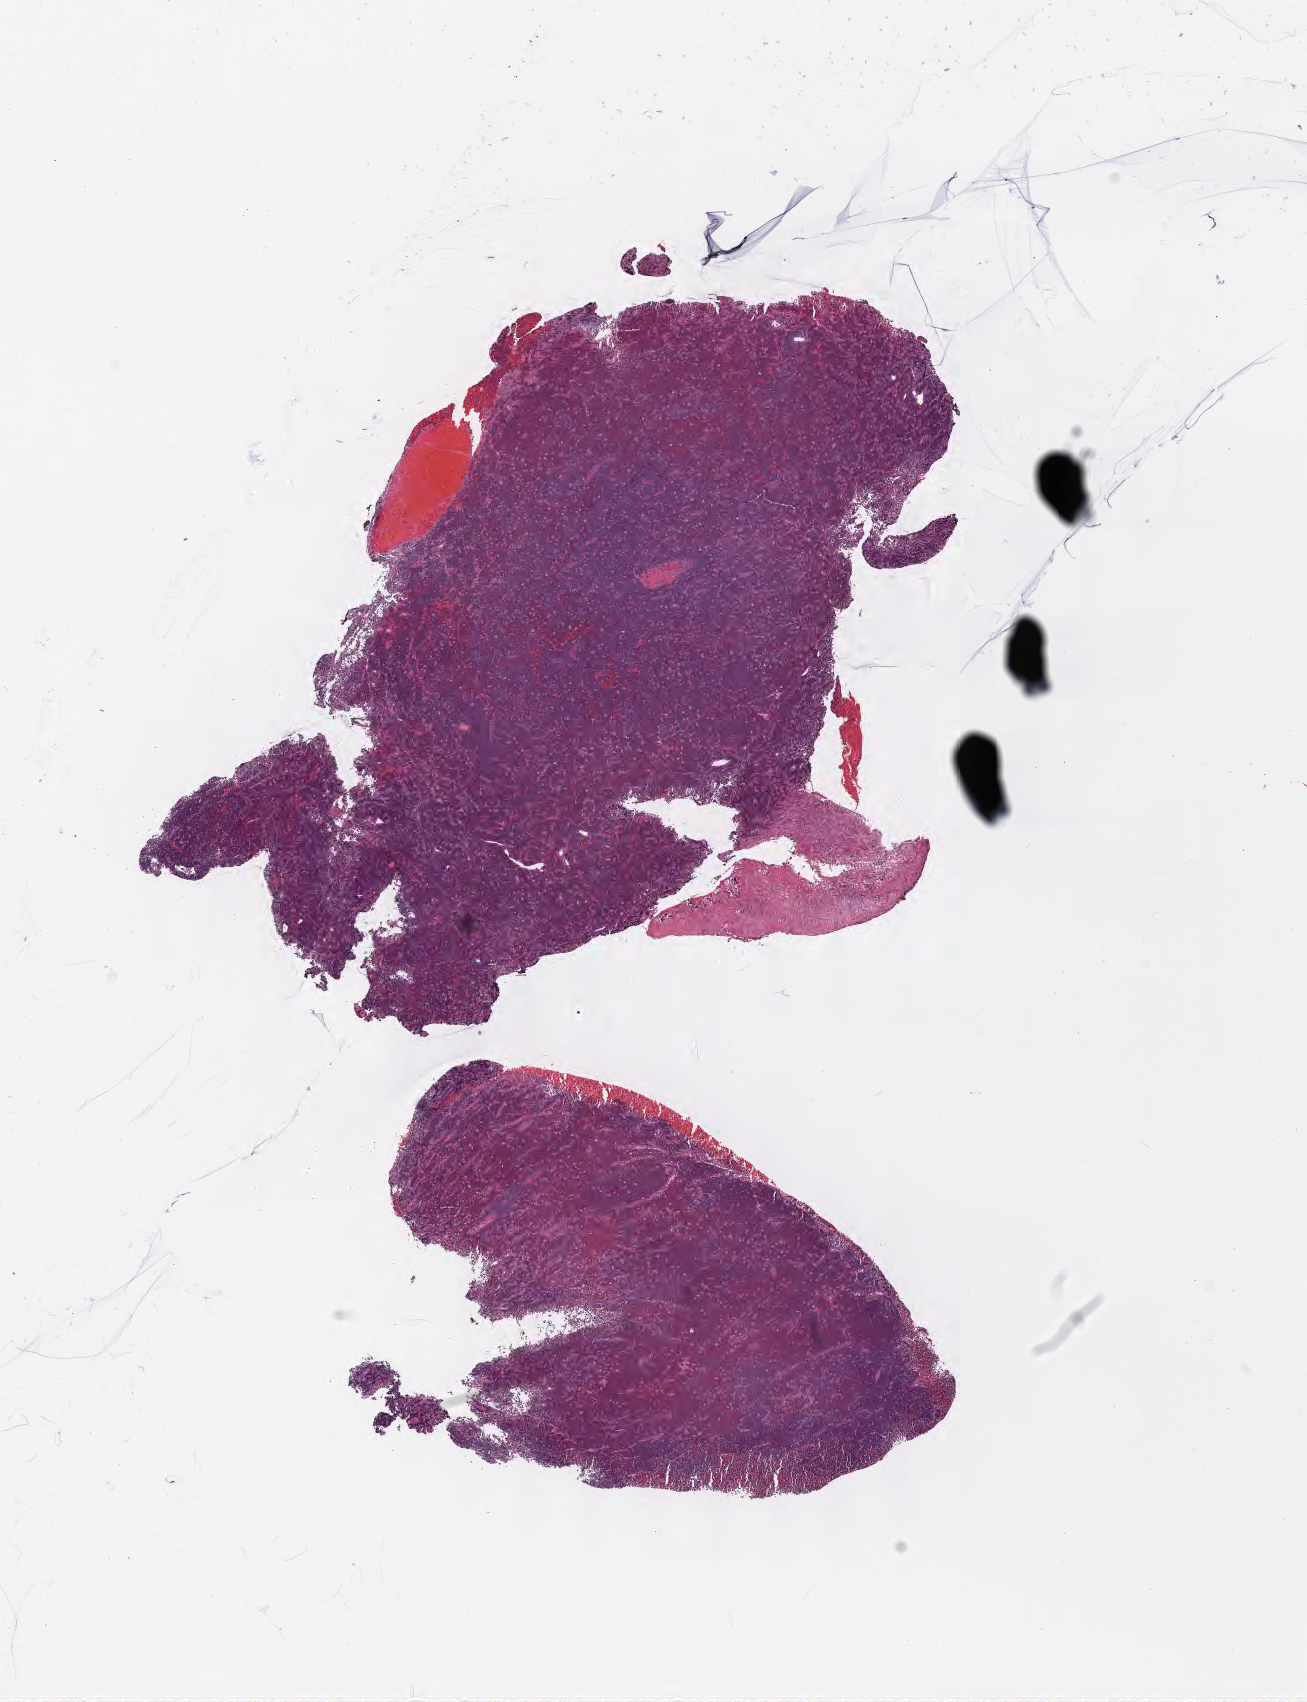
Digitized hematoxylin and eosin (H&E)-stained section, low-resolution overview of the scanned area, about 10.6 x 13.8 mm, tumor tissue, site: cranium. Male, age 2 years at initial diagnosis.
Diagnosis: Burkitt lymphoma, NOS.